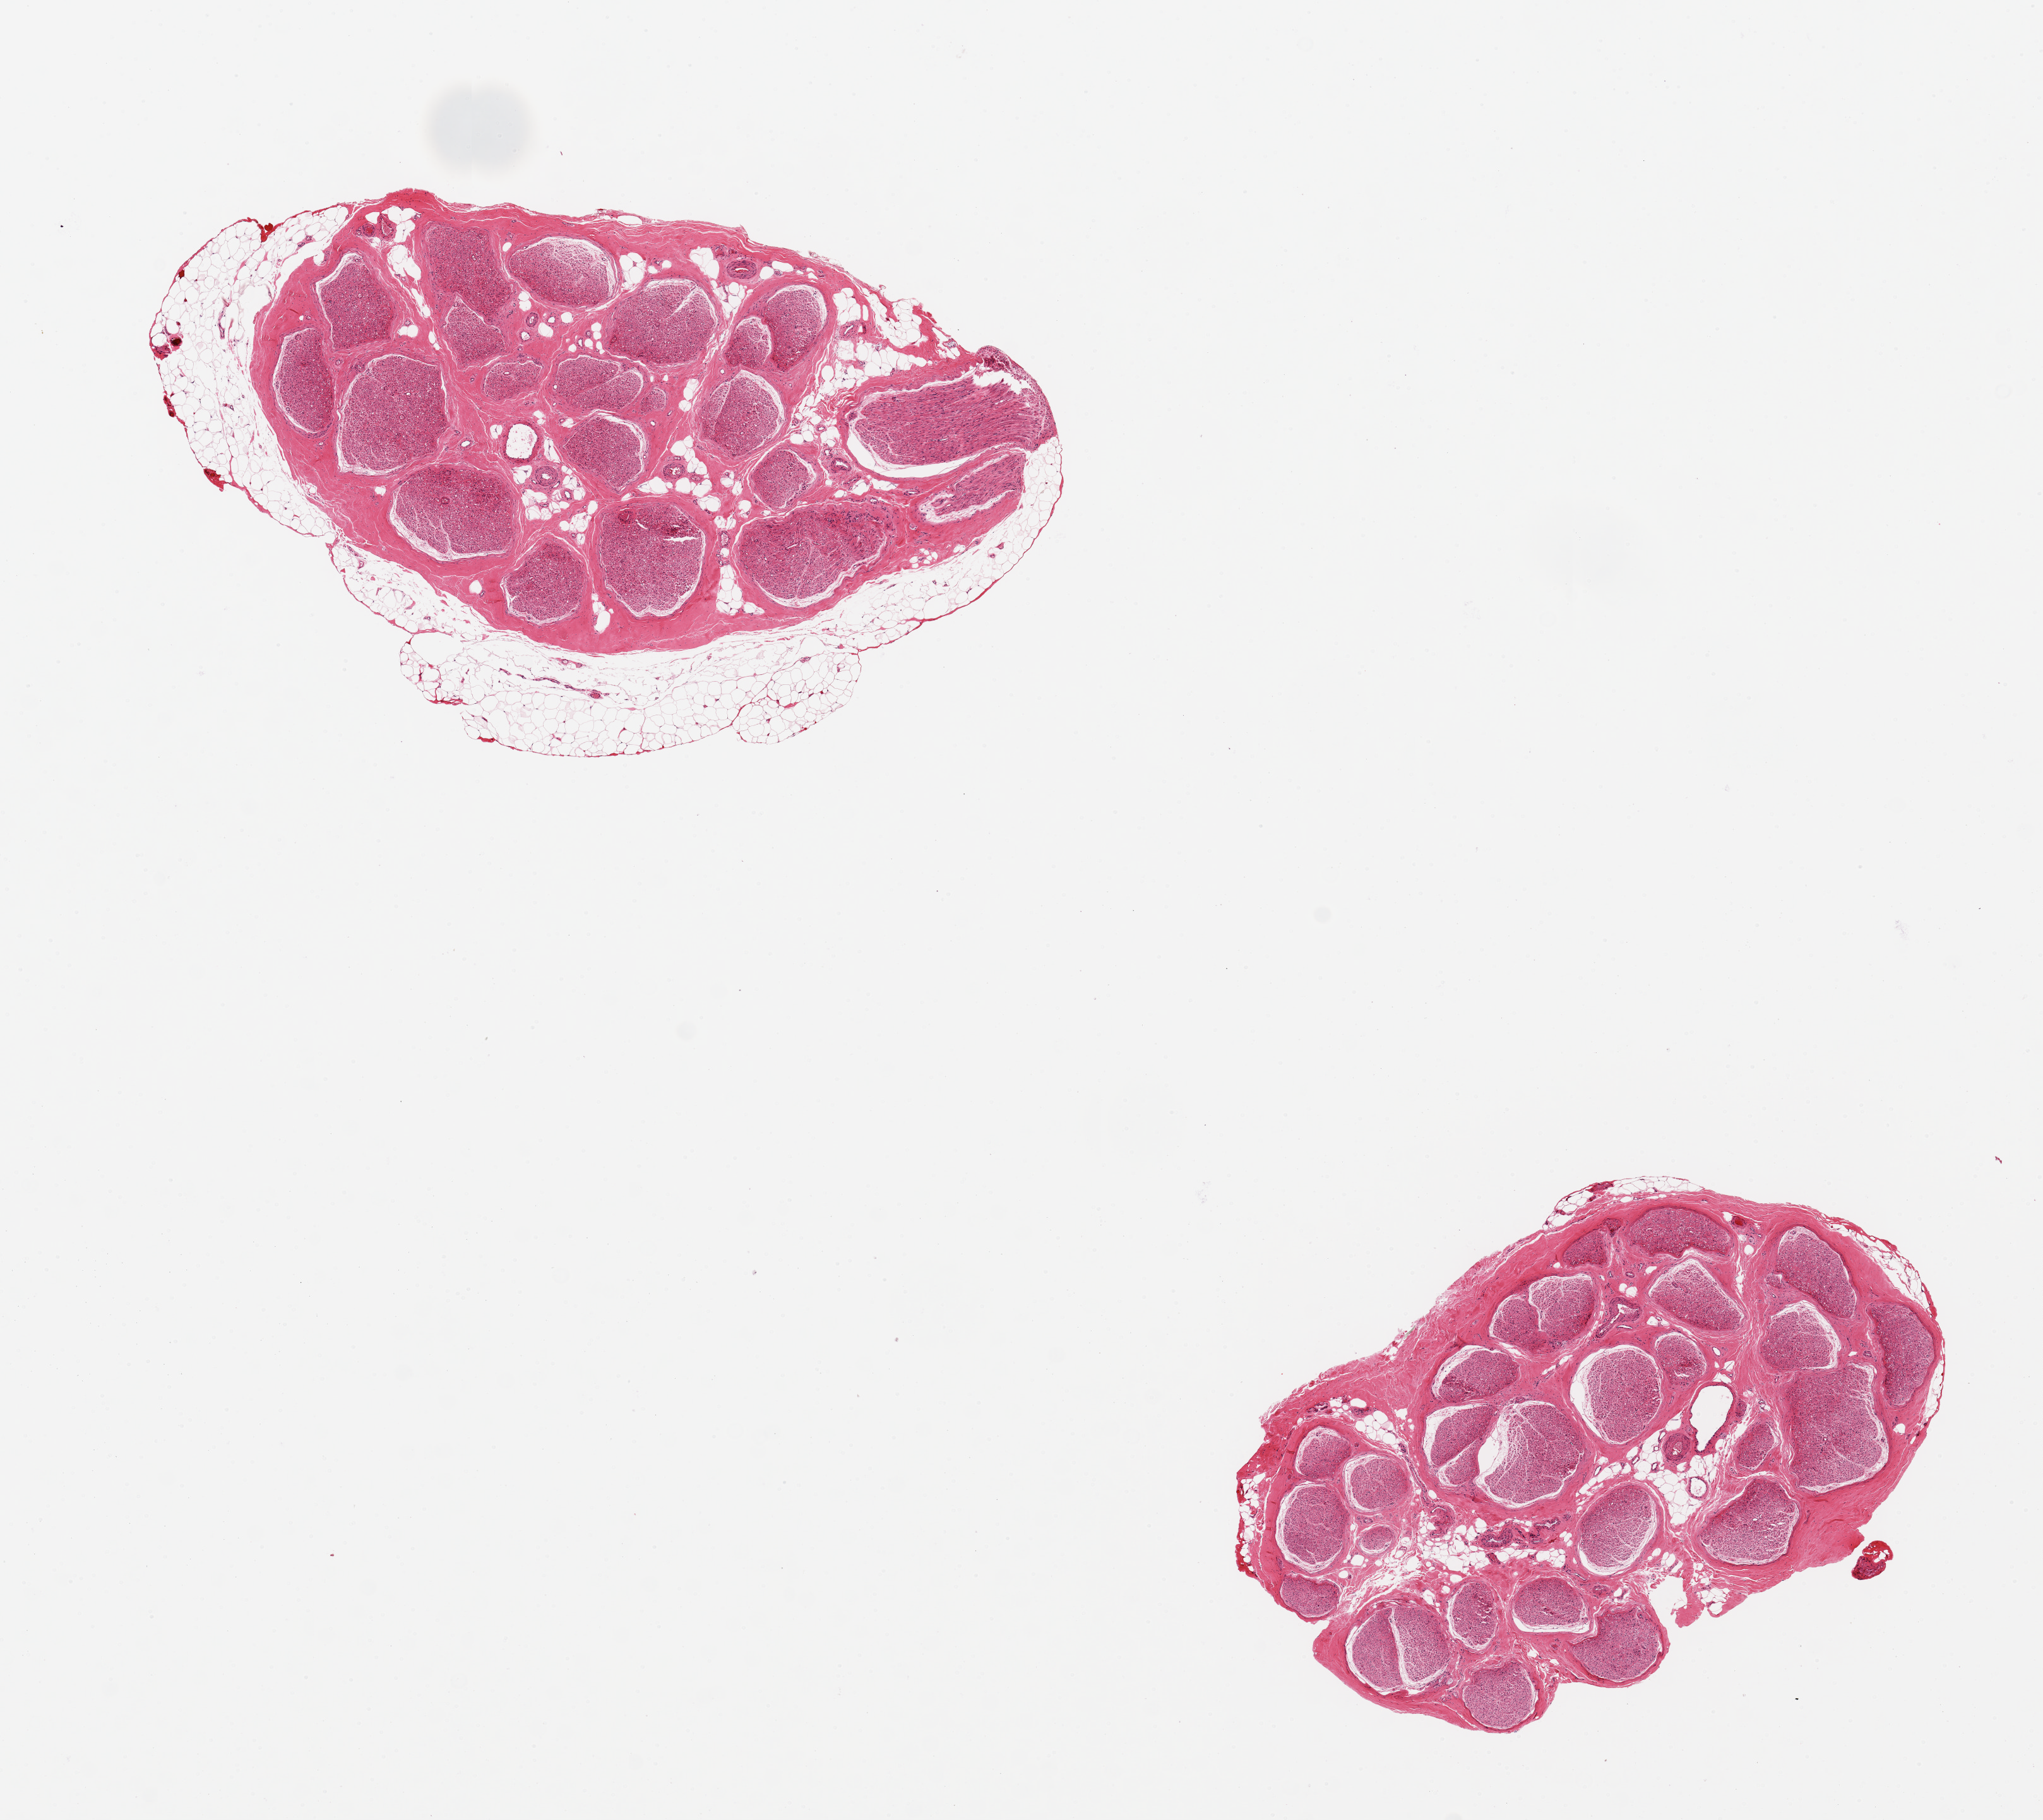
H&E whole-slide image — shown as a low-resolution overview of the whole scanned area (about 12.8 x 11.4 mm). PAXgene-fixed paraffin-embedded (PFPE) section. Sampled site (target tissue): tibial nerve. Tissue donor sample. Donor sex: male.
Reviewer comment on this tissue sample: 2 aliquots, ~4x2.5mm. One has rim of fat, ~0.5mm, discontinuous.